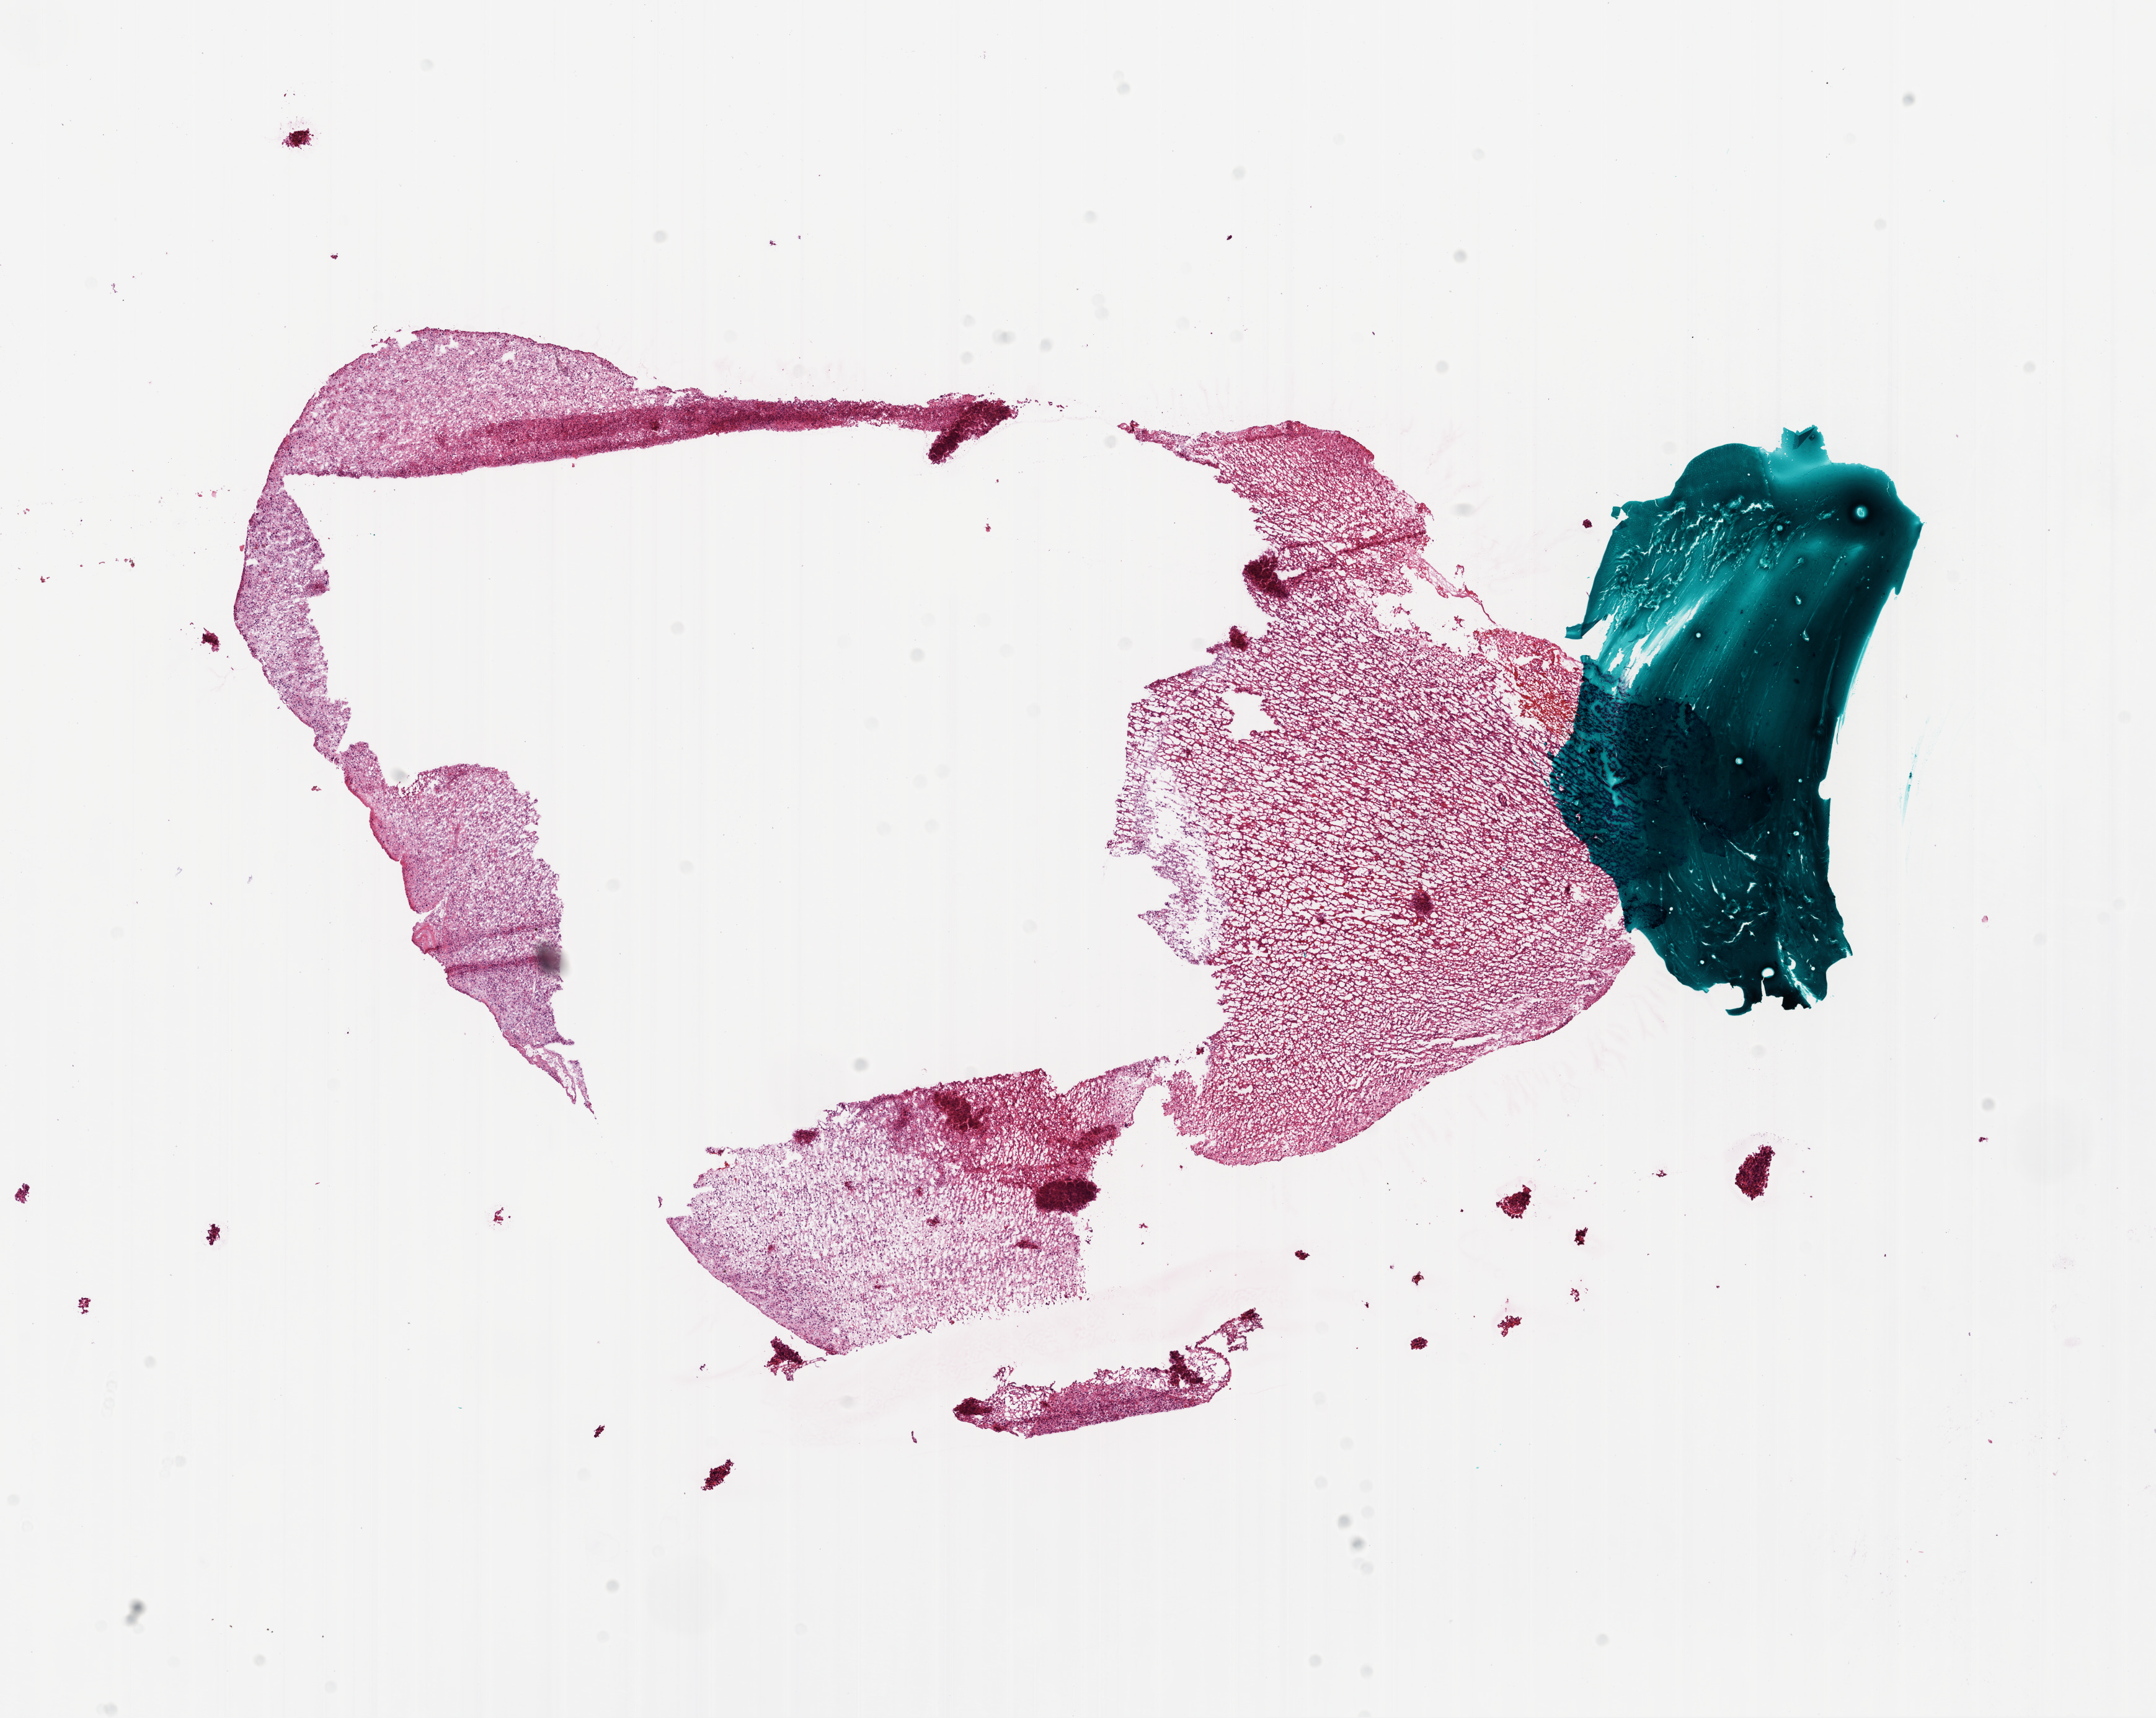
Whole-slide histology image, Hematoxylin and eosin (H&E) stained, shown as a low-resolution overview of the whole scanned area (about 14.0 x 11.2 mm, slide scanned at 20x), frozen section from the bottom of the tissue portion, sample: primary tumour, brain. Patient: female, age at initial diagnosis 36 years. Composition of this section per pathologist review: tumour cells 30%, tumour nuclei 100%, normal cells 0%, stromal cells 0%, necrosis 30%.
Diagnosis: Glioblastoma.